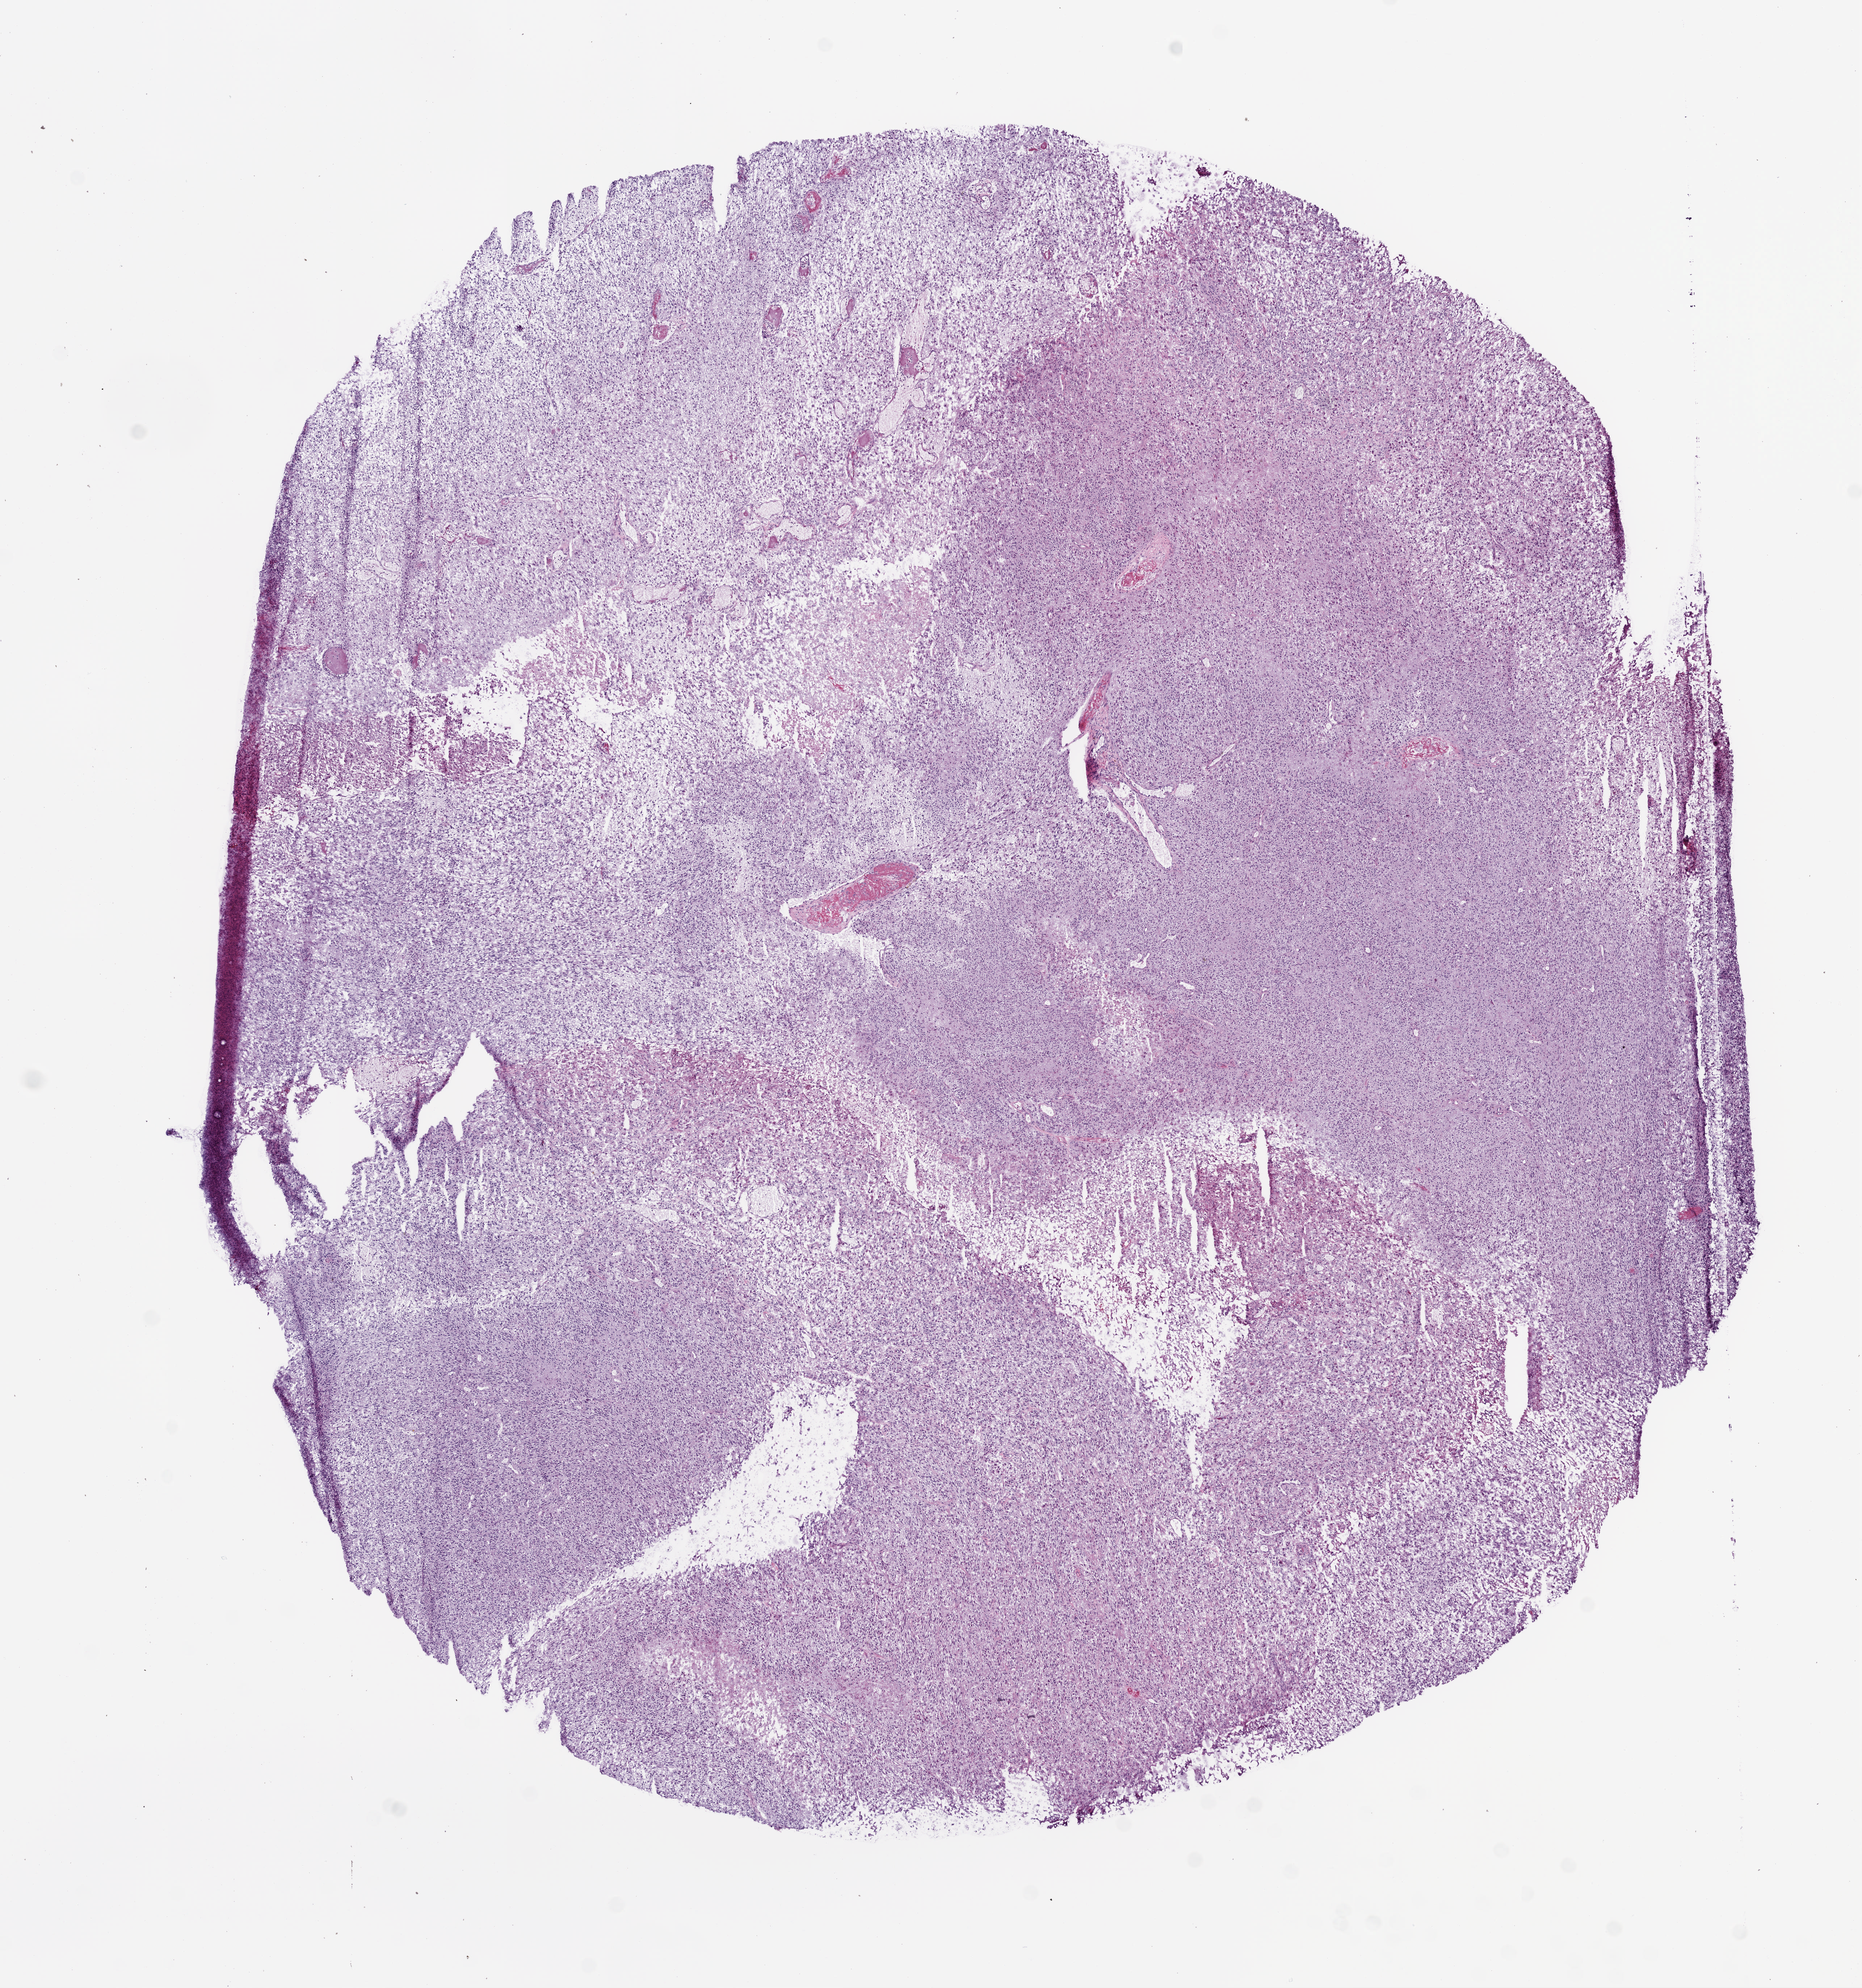
Whole-slide histology image, H&E-stained — the whole scanned area (about 10.3 x 11.0 mm) at the scan's own resolution, acquired at 5x; frozen section from the bottom of the tissue portion; primary tumour sample from the brain. Patient: female, age at initial diagnosis 75 years. Pathologist review of this section (percent, as recorded): tumour cells 90%, tumour nuclei 85%, normal cells 0%, stromal cells 0%, necrosis 10%.
• pathologic diagnosis: Glioblastoma